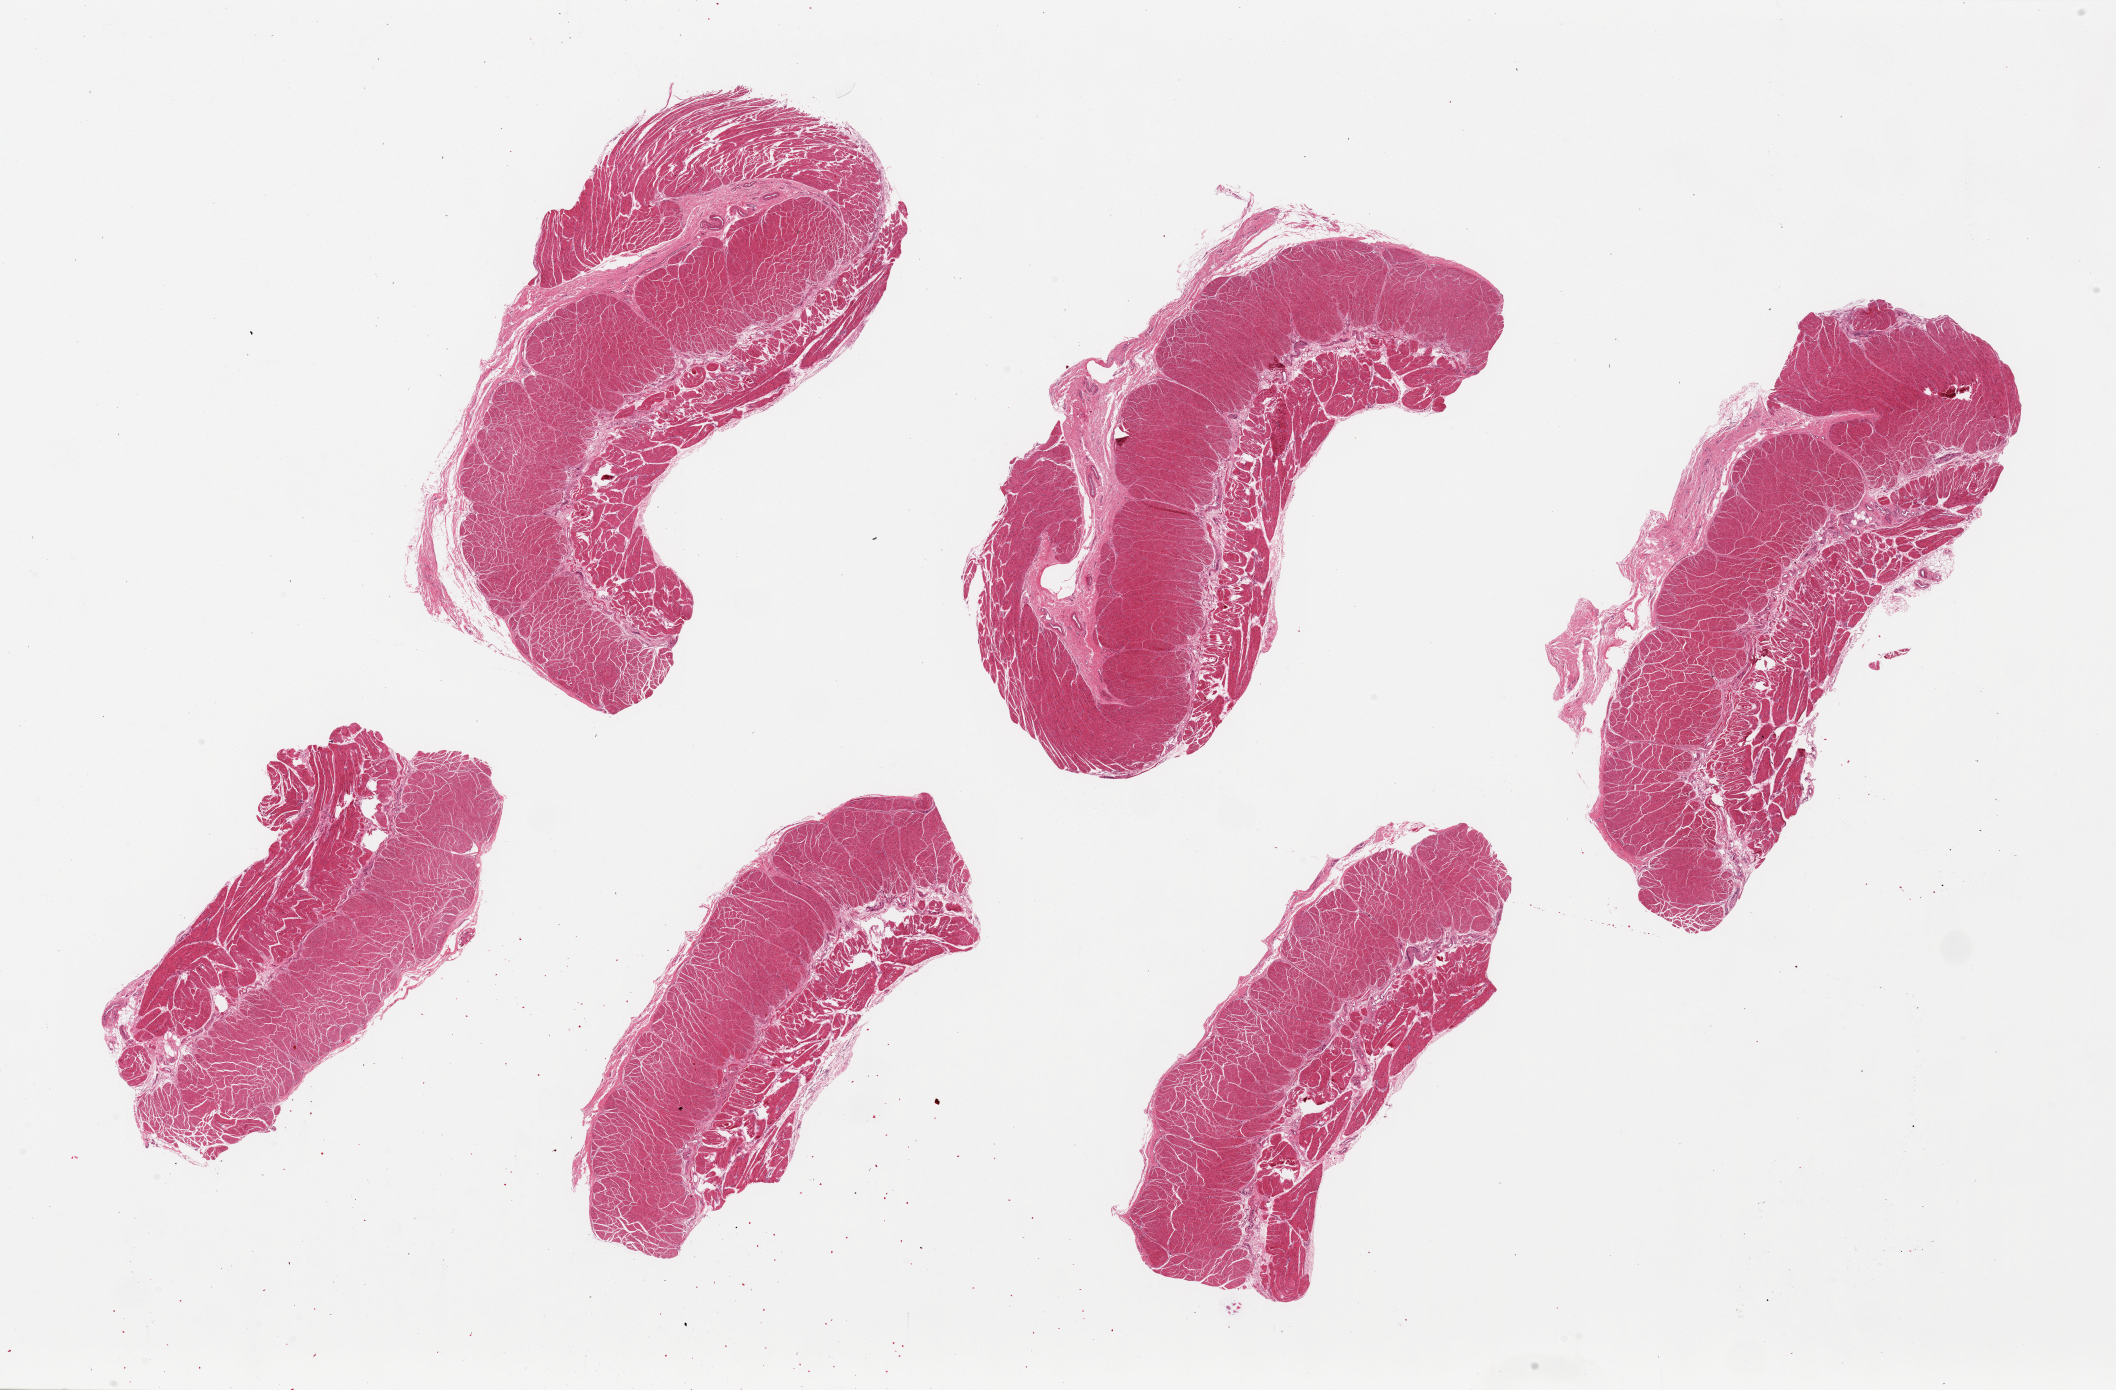
Whole-slide image, haematoxylin and eosin stain — a low-resolution overview of the entire scanned area, about 33.5 x 22.0 mm (acquisition: 20x scan), PAXgene-fixed paraffin-embedded (PFPE) section, target tissue: esophageal muscle, tissue donor sample. Male donor.
* reviewer comment on this tissue sample: 6 pieces, ~10x3mm